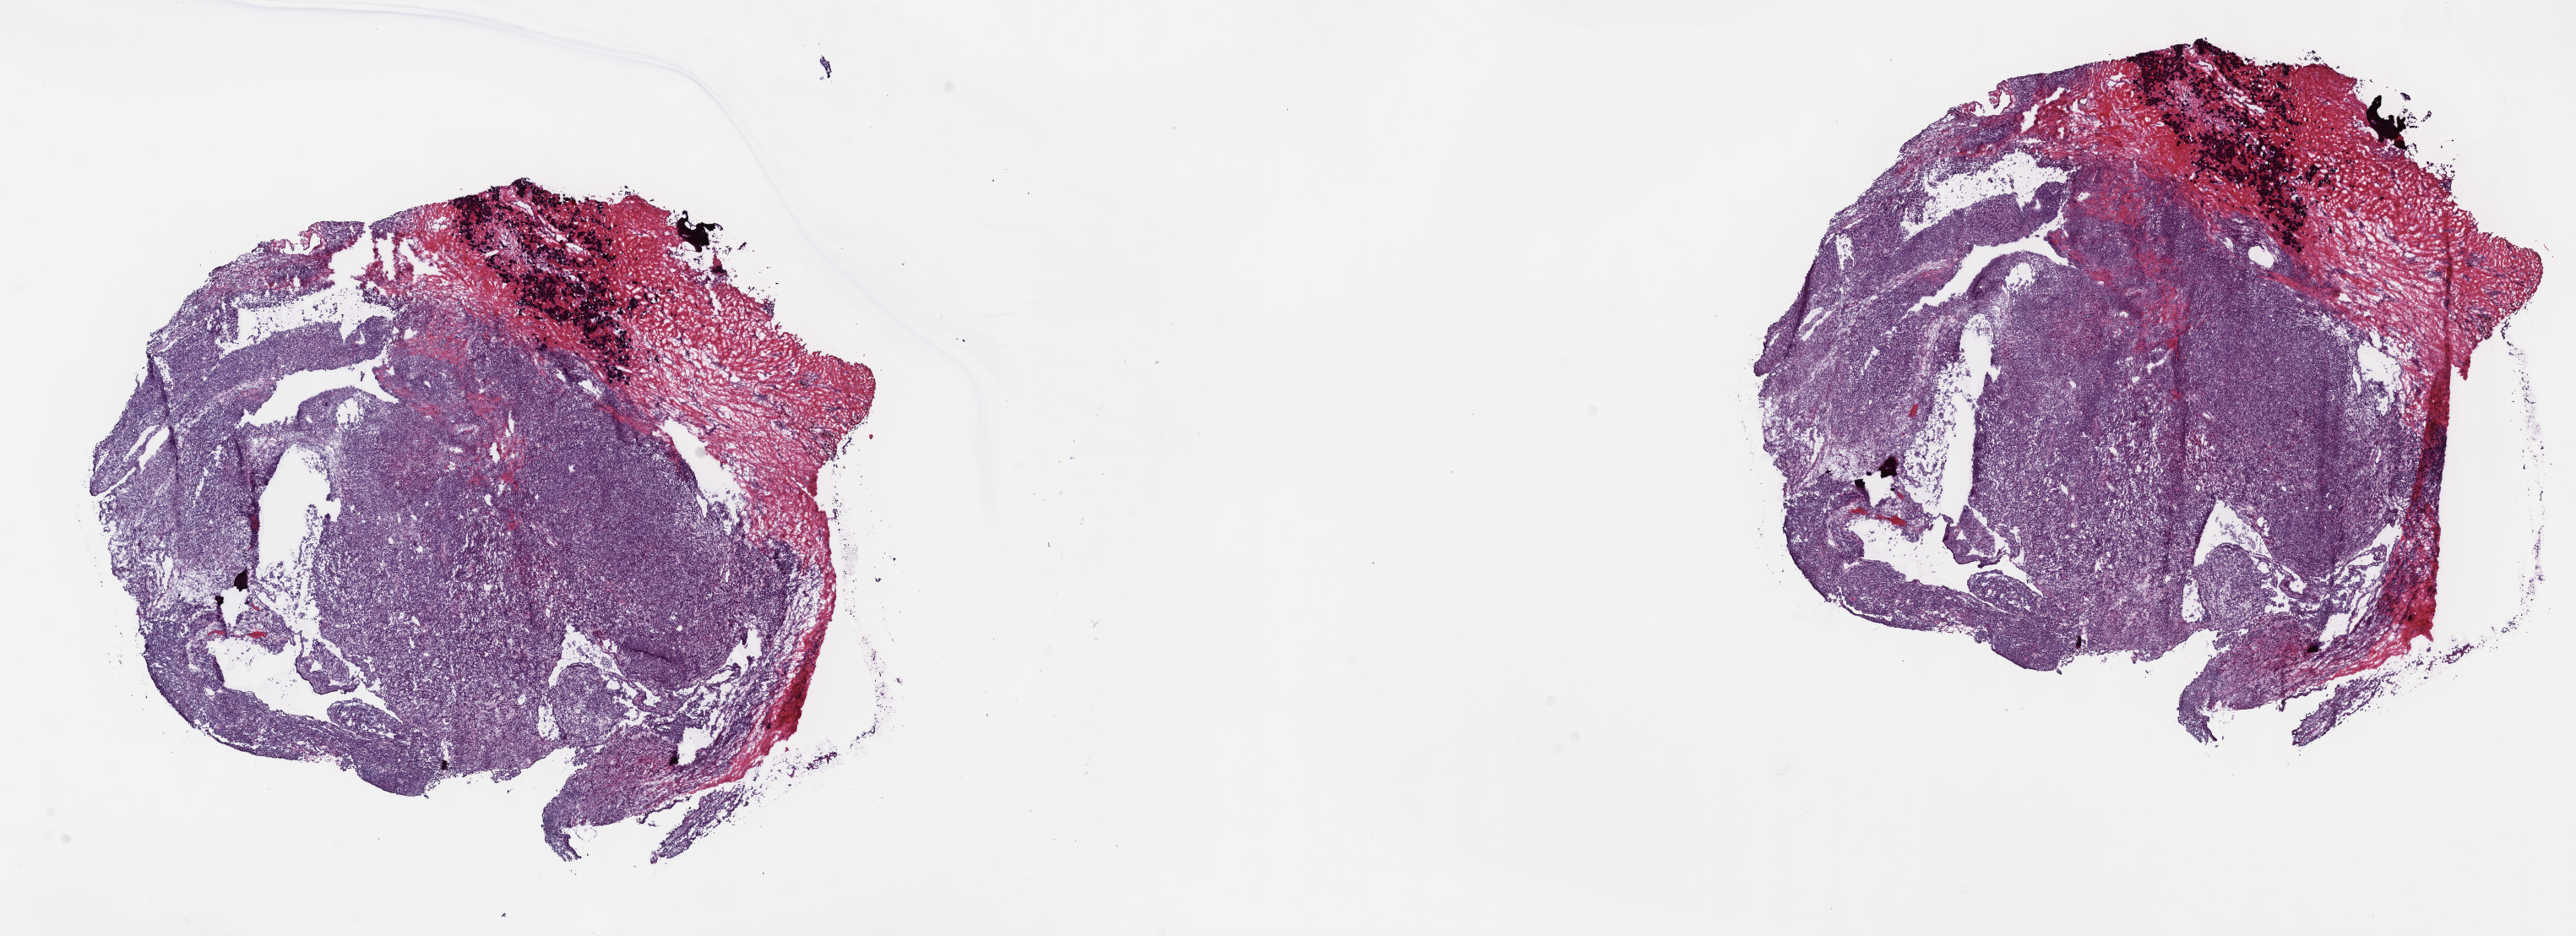
H&E-stained whole-slide image — shown as a low-resolution overview of the whole scanned area (about 24.7 x 9.0 mm), frozen section from the top of the tissue portion, sample: primary tumour, mesothelium. Male, age 68 years at initial diagnosis. Pathologist review of this section (percent, as recorded): tumour cells 70%, tumour nuclei 70%, normal cells 0%, stromal cells 20%, necrosis 10%. Inflammatory infiltration, as recorded: lymphocyte infiltration 60%, monocyte infiltration 10%, neutrophil infiltration 10%.
Histologic diagnosis: Mesothelioma, biphasic, malignant (pleura, NOS). AJCC pathologic stage: III (7th edition).